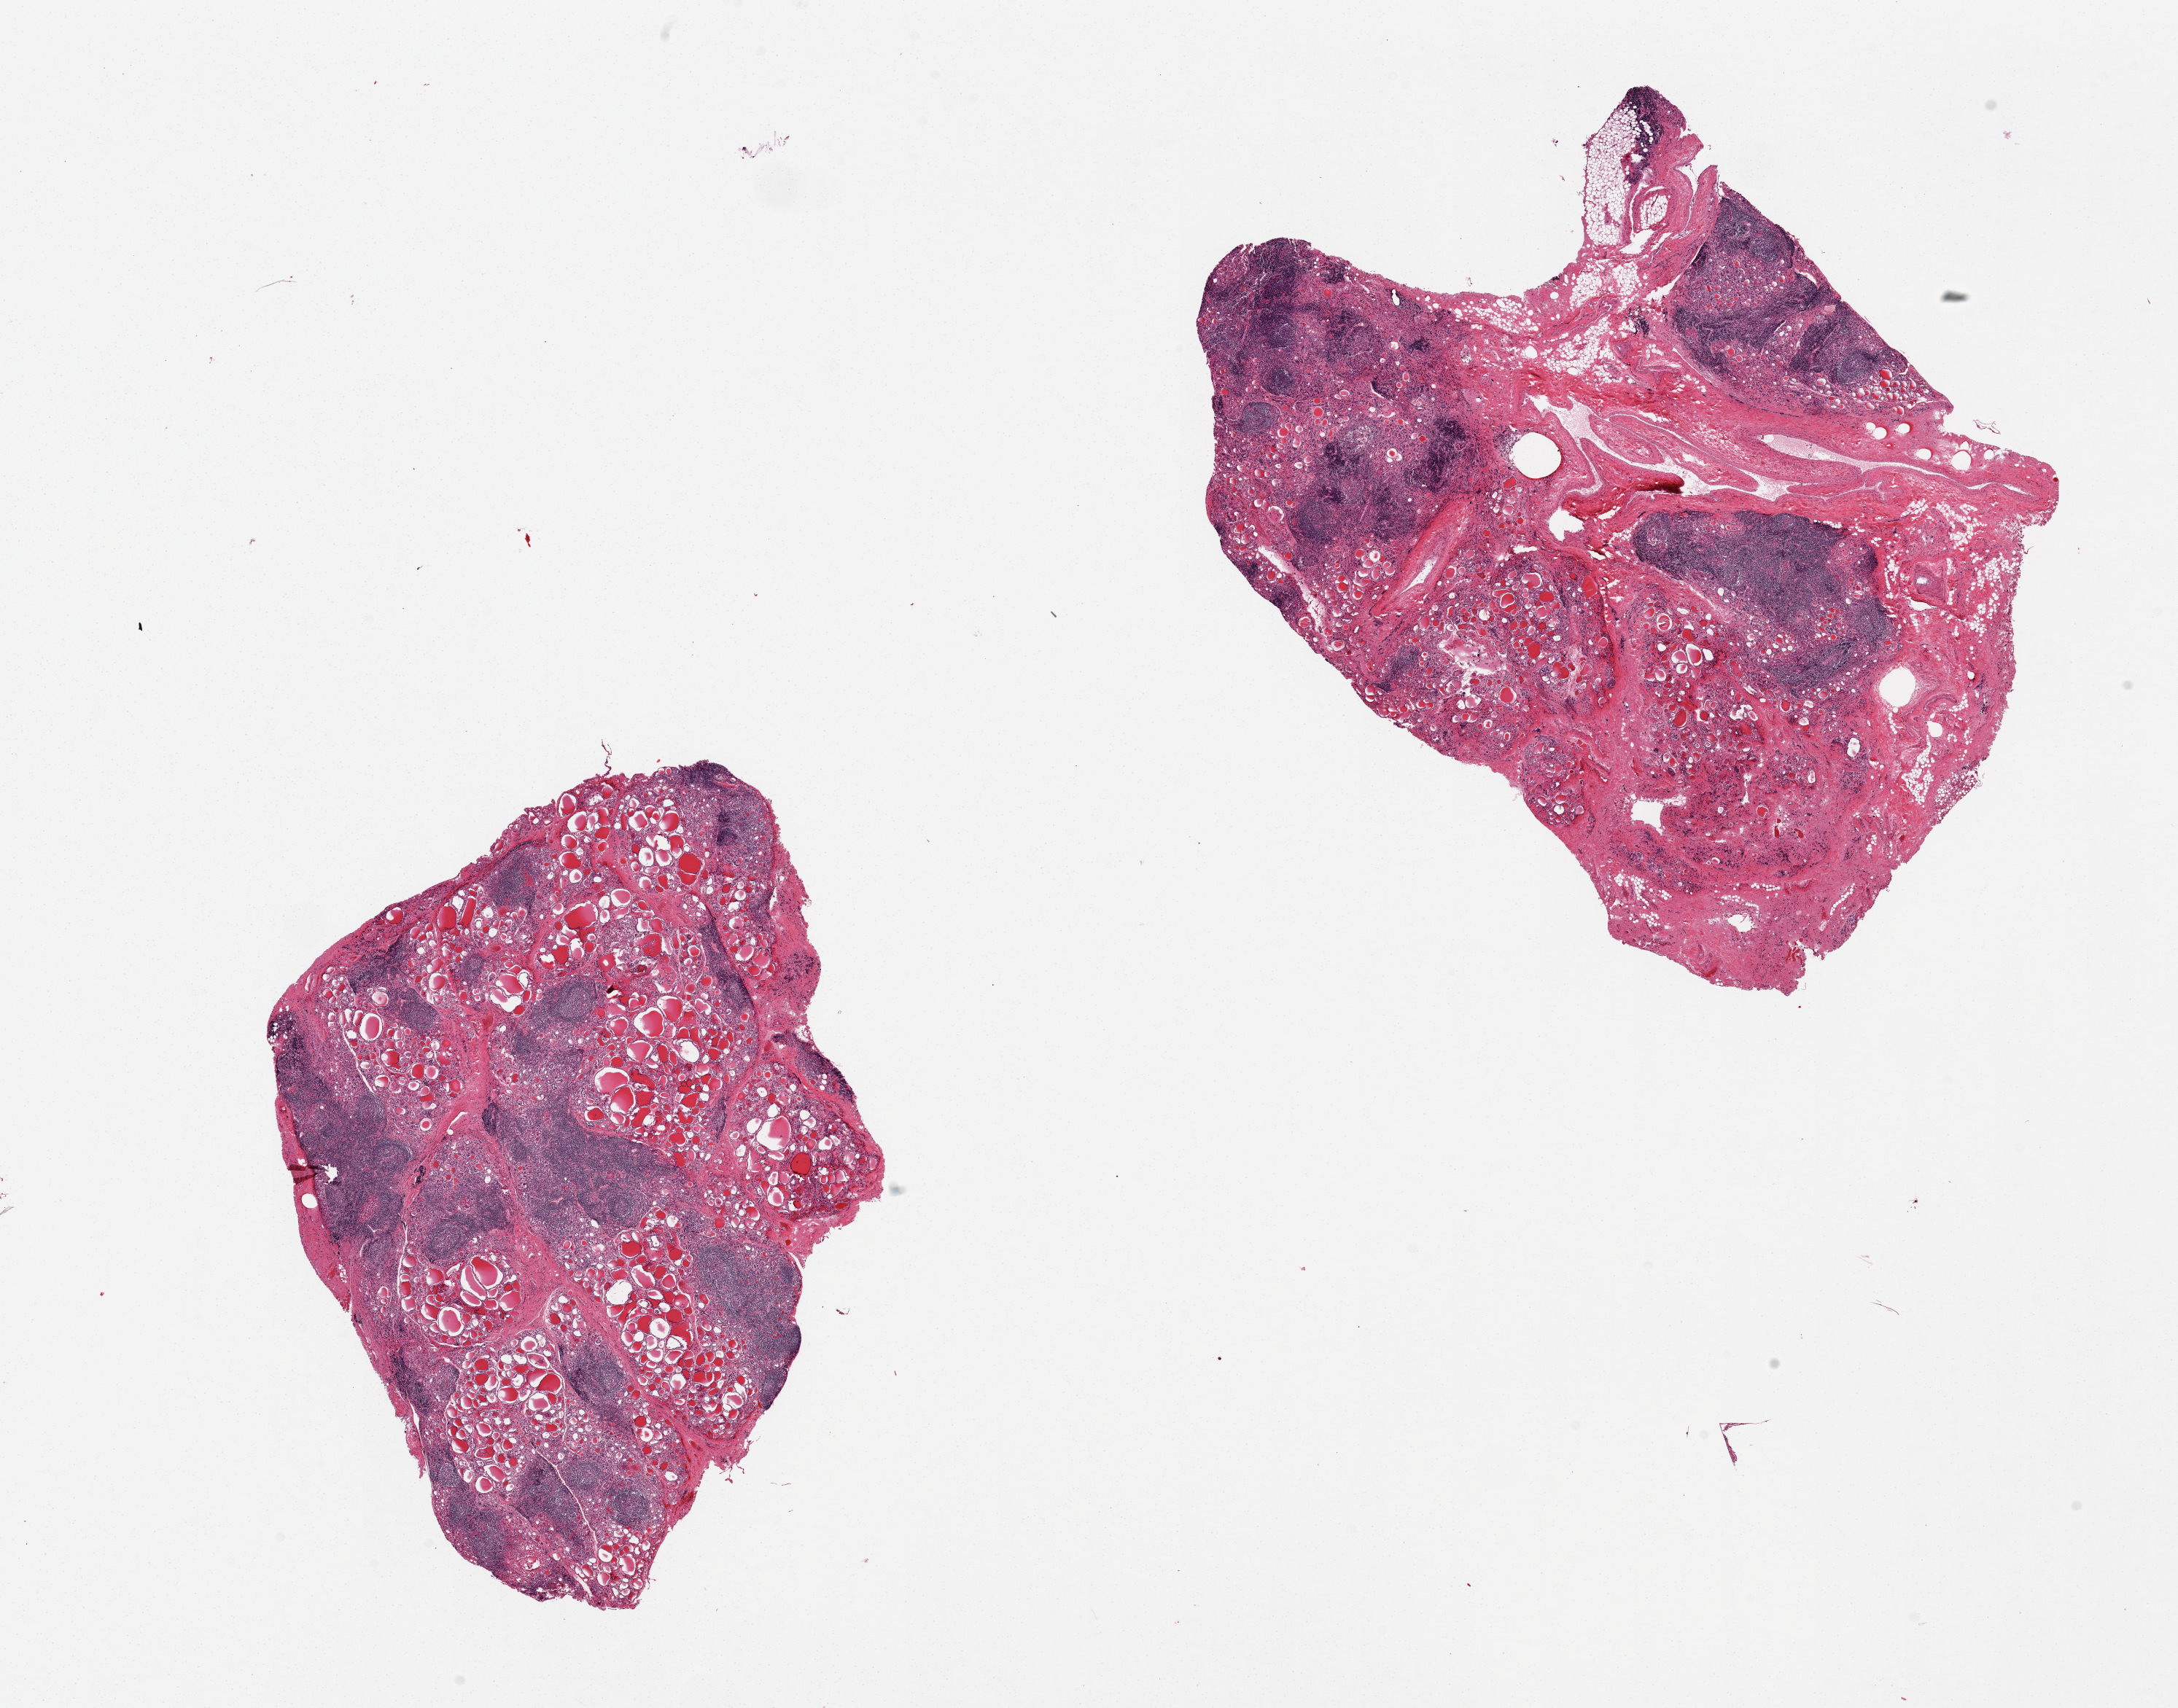
Whole-slide image, haematoxylin and eosin stain, a low-resolution overview of the entire scanned area, about 23.6 x 18.5 mm. PAXgene-fixed, paraffin-embedded tissue. Section of thyroid (target tissue). Donor tissue sample. Female donor.
- review note (as recorded): 2 pieces; Late stage Hashimoto's thyroiditis with regressive/fibrotic changes, prominent lymphoid follicles